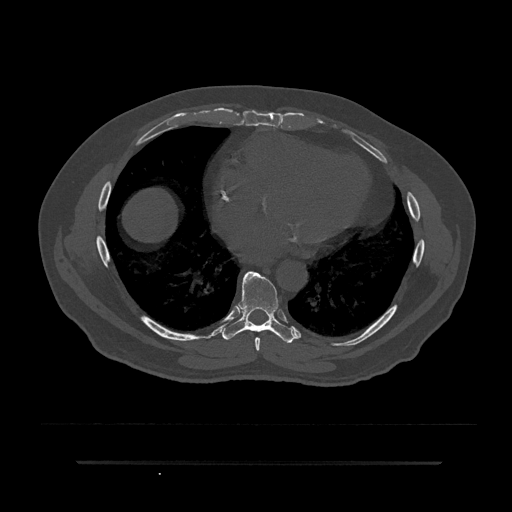
CT including the spine, one axial slice. Slice 440 of 797 in the series (ordered by position). Reconstruction kernel Br40s/3. Bone window (W 1800 / L 400 HU). 0.5 mm slice thickness. 512 × 512 image matrix. Male patient, age 59 years. From the clinical record (not read from this slice): primary cancer: bile ducts.
Annotated regions visible in this slice (semi-automatic segmentation, software-assisted and operator-edited):
- T7 vertebra: bounding box [x1, y1, x2, y2] px = [255, 337, 260, 351]
- T8 vertebra: [222, 271, 295, 343]